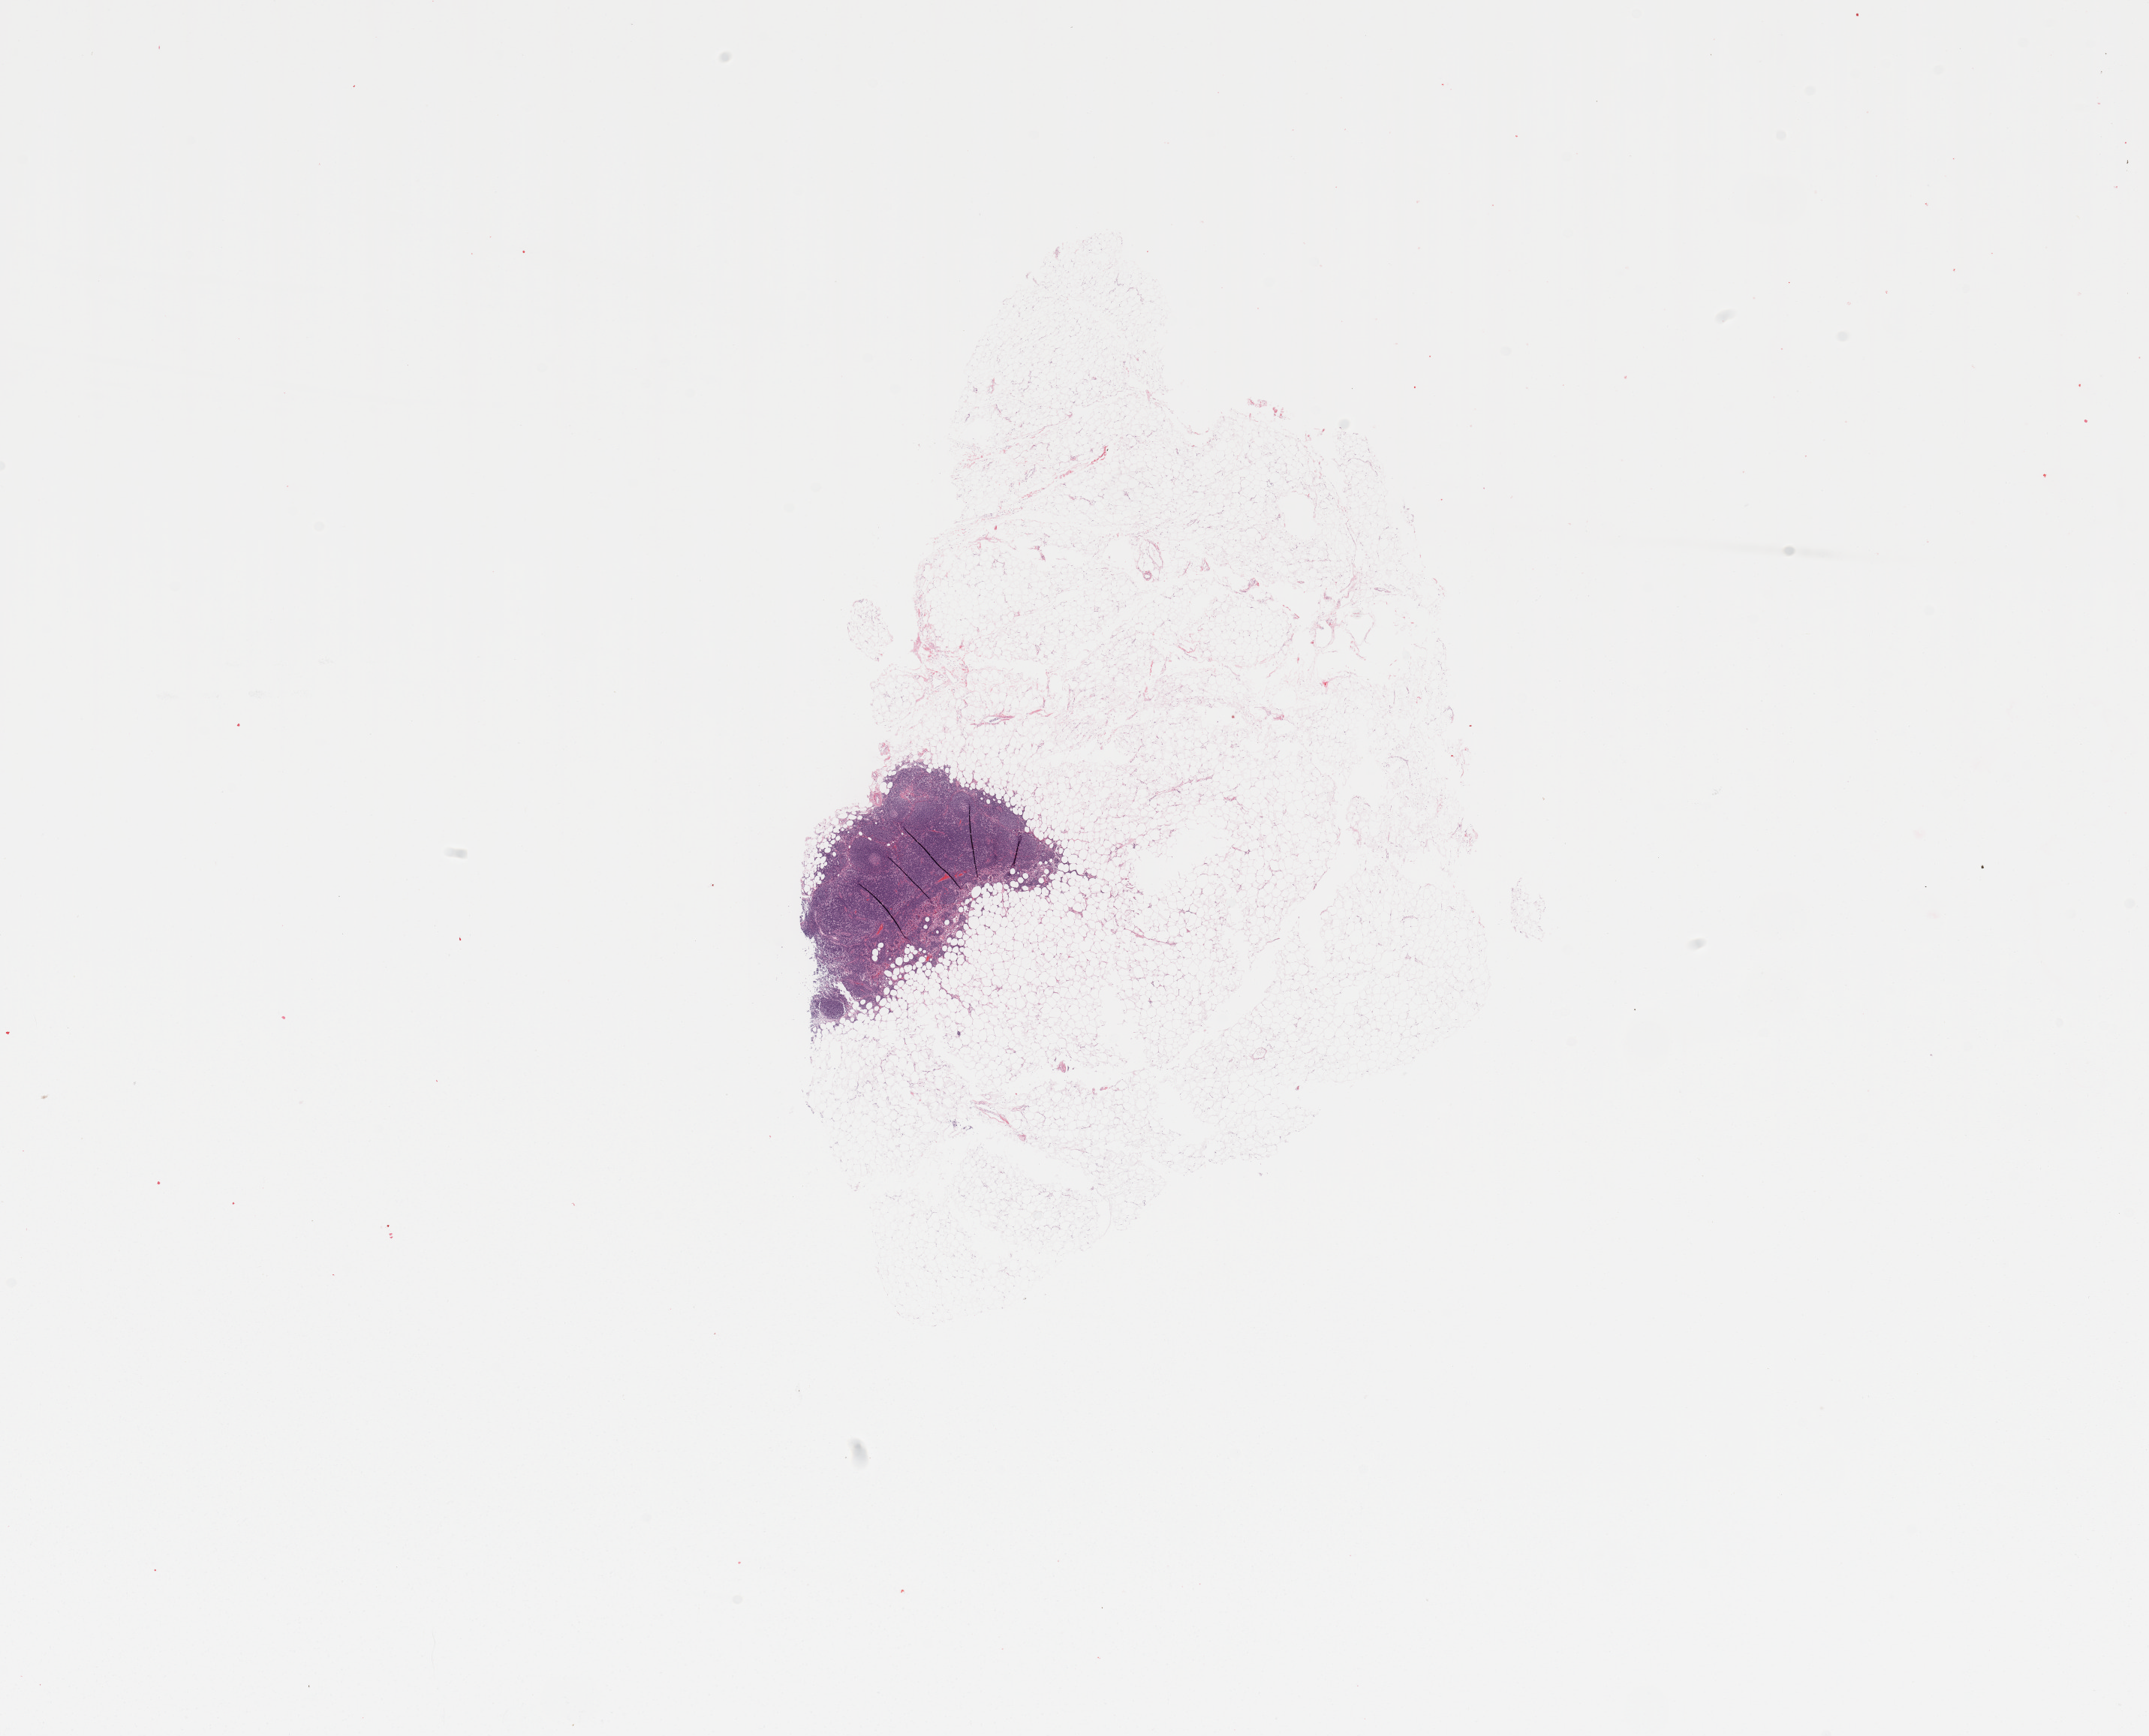
Hematoxylin and eosin (H&E) stained whole-slide image, shown as a low-resolution overview of the whole scanned area (about 22.6 x 18.3 mm), pancreas, normal (non-tumour) tissue. Female, 51 y/o.
This section: normal (non-tumour) tissue from the same patient. Patient diagnosis: Infiltrating duct carcinoma, NOS.